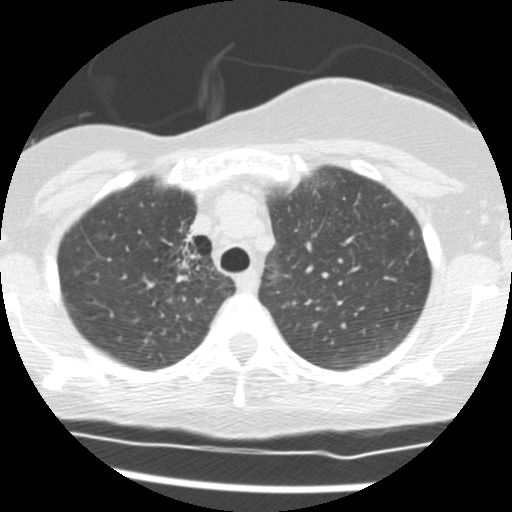
Low-dose screening chest CT, axial slice. Second screening round (one year after baseline). Lung window (W 1500 / L -600 HU). 2.5 mm slice thickness. 512 × 512 image matrix, field of view 296 × 296 mm. Female participant, aged 56 years at enrolment.
Lesion marked by an expert reader, bounding box <156,220,217,288> (left, top, right, bottom; pixels). The screening reader recorded 2 non-calcified nodules or masses ≥4 mm on this exam; which of them this box marks is not recorded. Later outcome: lung cancer diagnosed 675 days after this screen — adenocarcinoma, NOS, right upper lobe, stage IIIB (AJCC 6th edition), 8 mm at pathology.